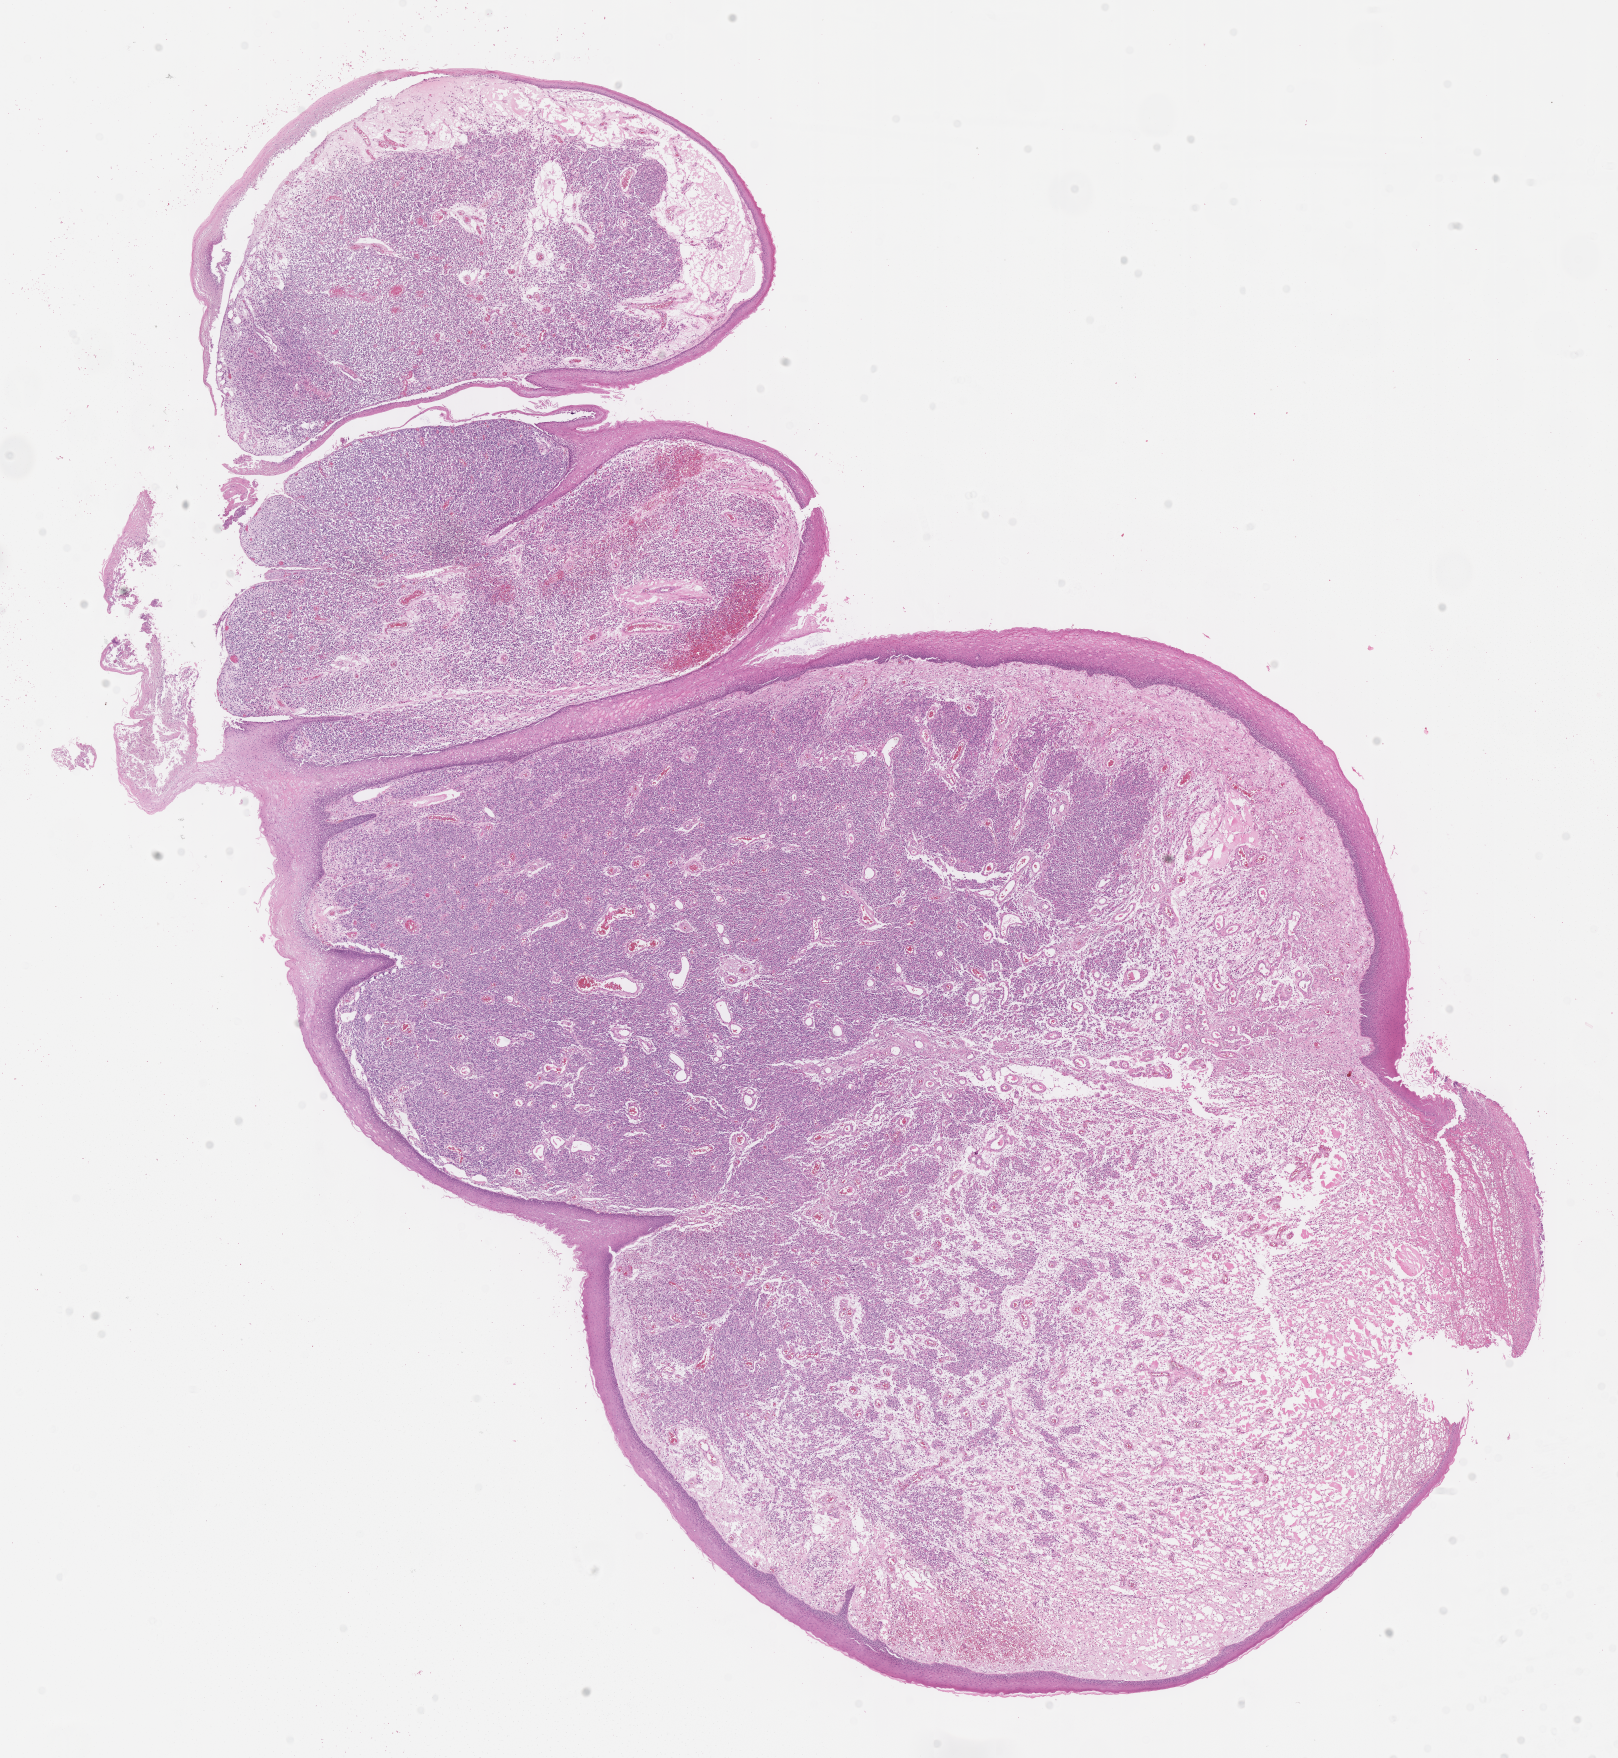
Digitized hematoxylin and eosin (H&E)-stained section of tumor tissue, whole scanned area (about 13.1 x 14.2 mm) shown as a low-resolution overview; FFPE section; sample anatomic site: uvula. Female patient, age at diagnosis 2.1 years.
• primary site (case record): oropharynx
• stage (as recorded): 1
• metastatic status at presentation (as recorded): non-metastatic
• diagnosis: rhabdomyosarcoma; histological classification: embryonal rhabdomyosarcoma